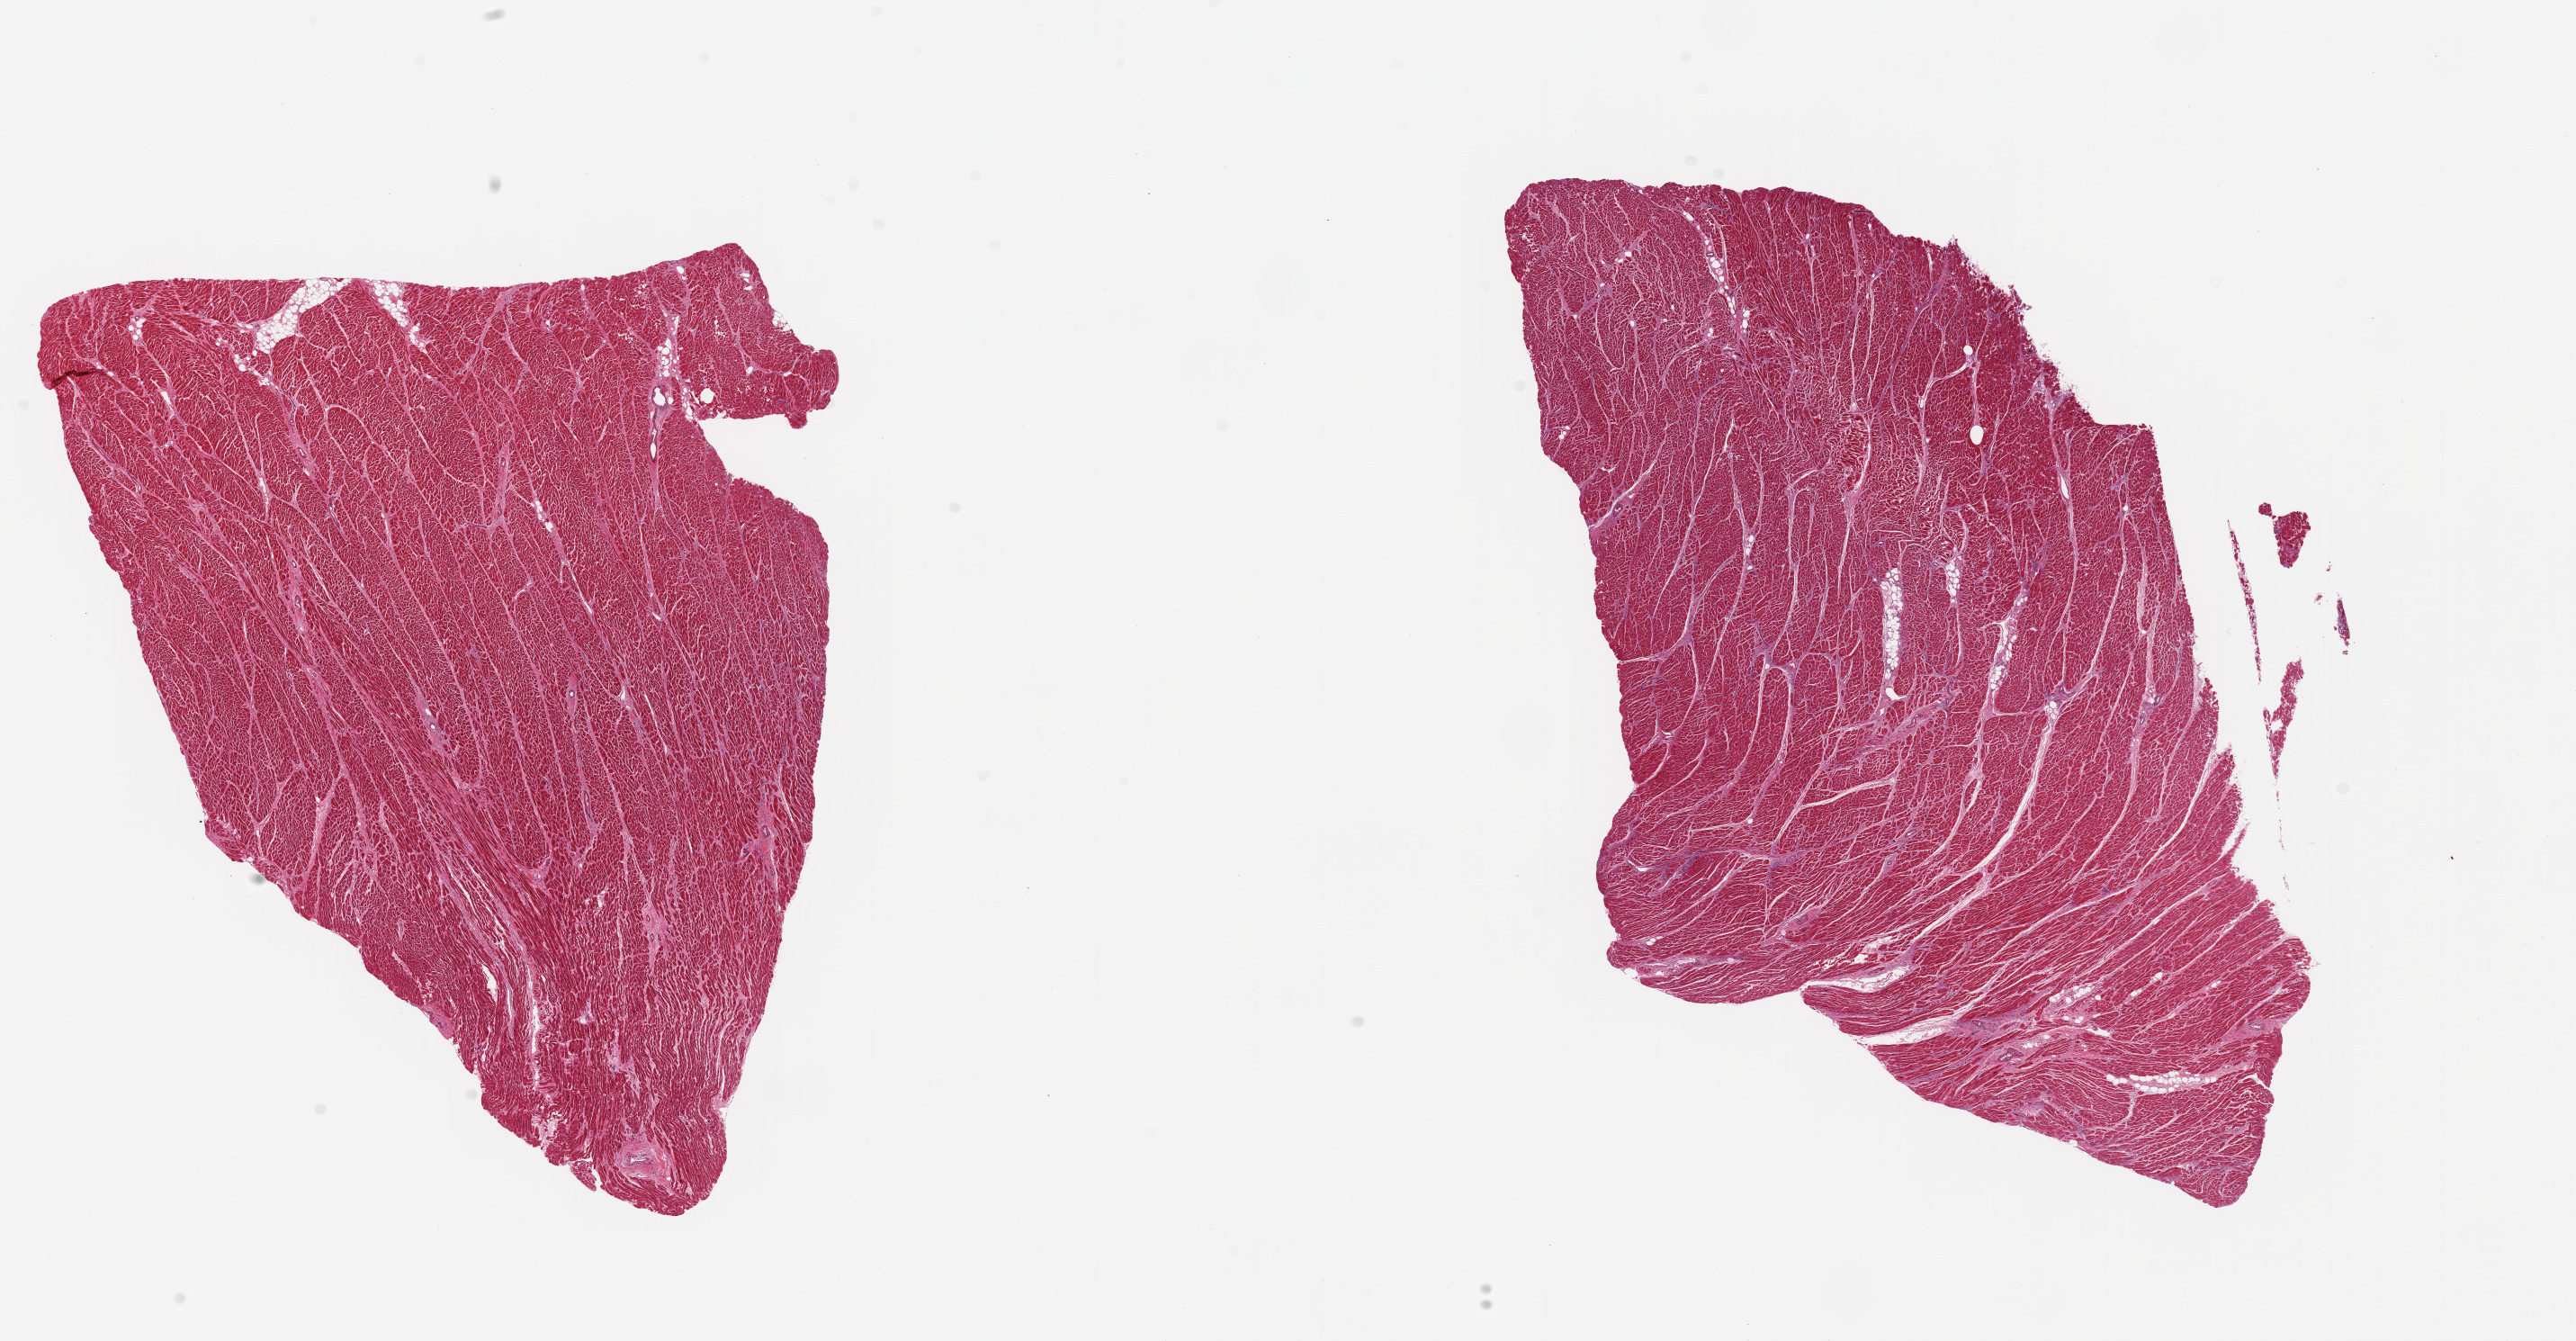
Digitized hematoxylin and eosin (H&E)-stained section, low-resolution overview of the scanned area, about 22.6 x 11.8 mm (slide scanned at 20x), PAXgene-fixed, paraffin-embedded tissue, target tissue: heart, donor tissue sample. Male donor.
Review note (as recorded): 2 pieces; scattered areas of fibrosis <5%; enlarged nuclei.